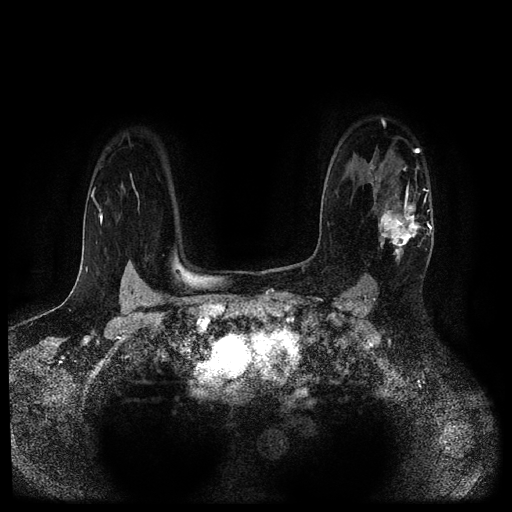
Breast MRI (dynamic contrast-enhanced, multi-phase), one axial slice; position 78 of 116 along the scan axis; dynamic contrast-enhanced series, time point 2 of 5 at this slice position (early post-contrast); 1.5 T; TE 2.7 ms, TR 5.4 ms; 512 × 512 image matrix, field of view 330 × 330 mm. Patient: female, 43 years.
Annotated regions visible in this slice (semi-automatically segmented with operator editing):
- breast lesion (labelled 'tumour' in the annotation; benign lesions carry a separate 'benign' label): bounding box <377,182,424,265> (left, top, right, bottom; pixels)